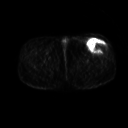
FDG PET of an extremity soft-tissue mass (from a PET/CT study), one axial slice. Position 244 of 267 along the scan axis. 128 × 128 image matrix. Male patient, age 64 years. Case-level facts recorded for this patient, not image findings: histological type: extraskeletal osteosarcoma; grade: high; site of the primary tumour: thigh.
Structures marked on this image (expert contour drawn on MRI and transferred to this co-registered scan by the dataset authors):
- gross tumour volume (mass): bounding box <88,40,107,53> (left, top, right, bottom; pixels)